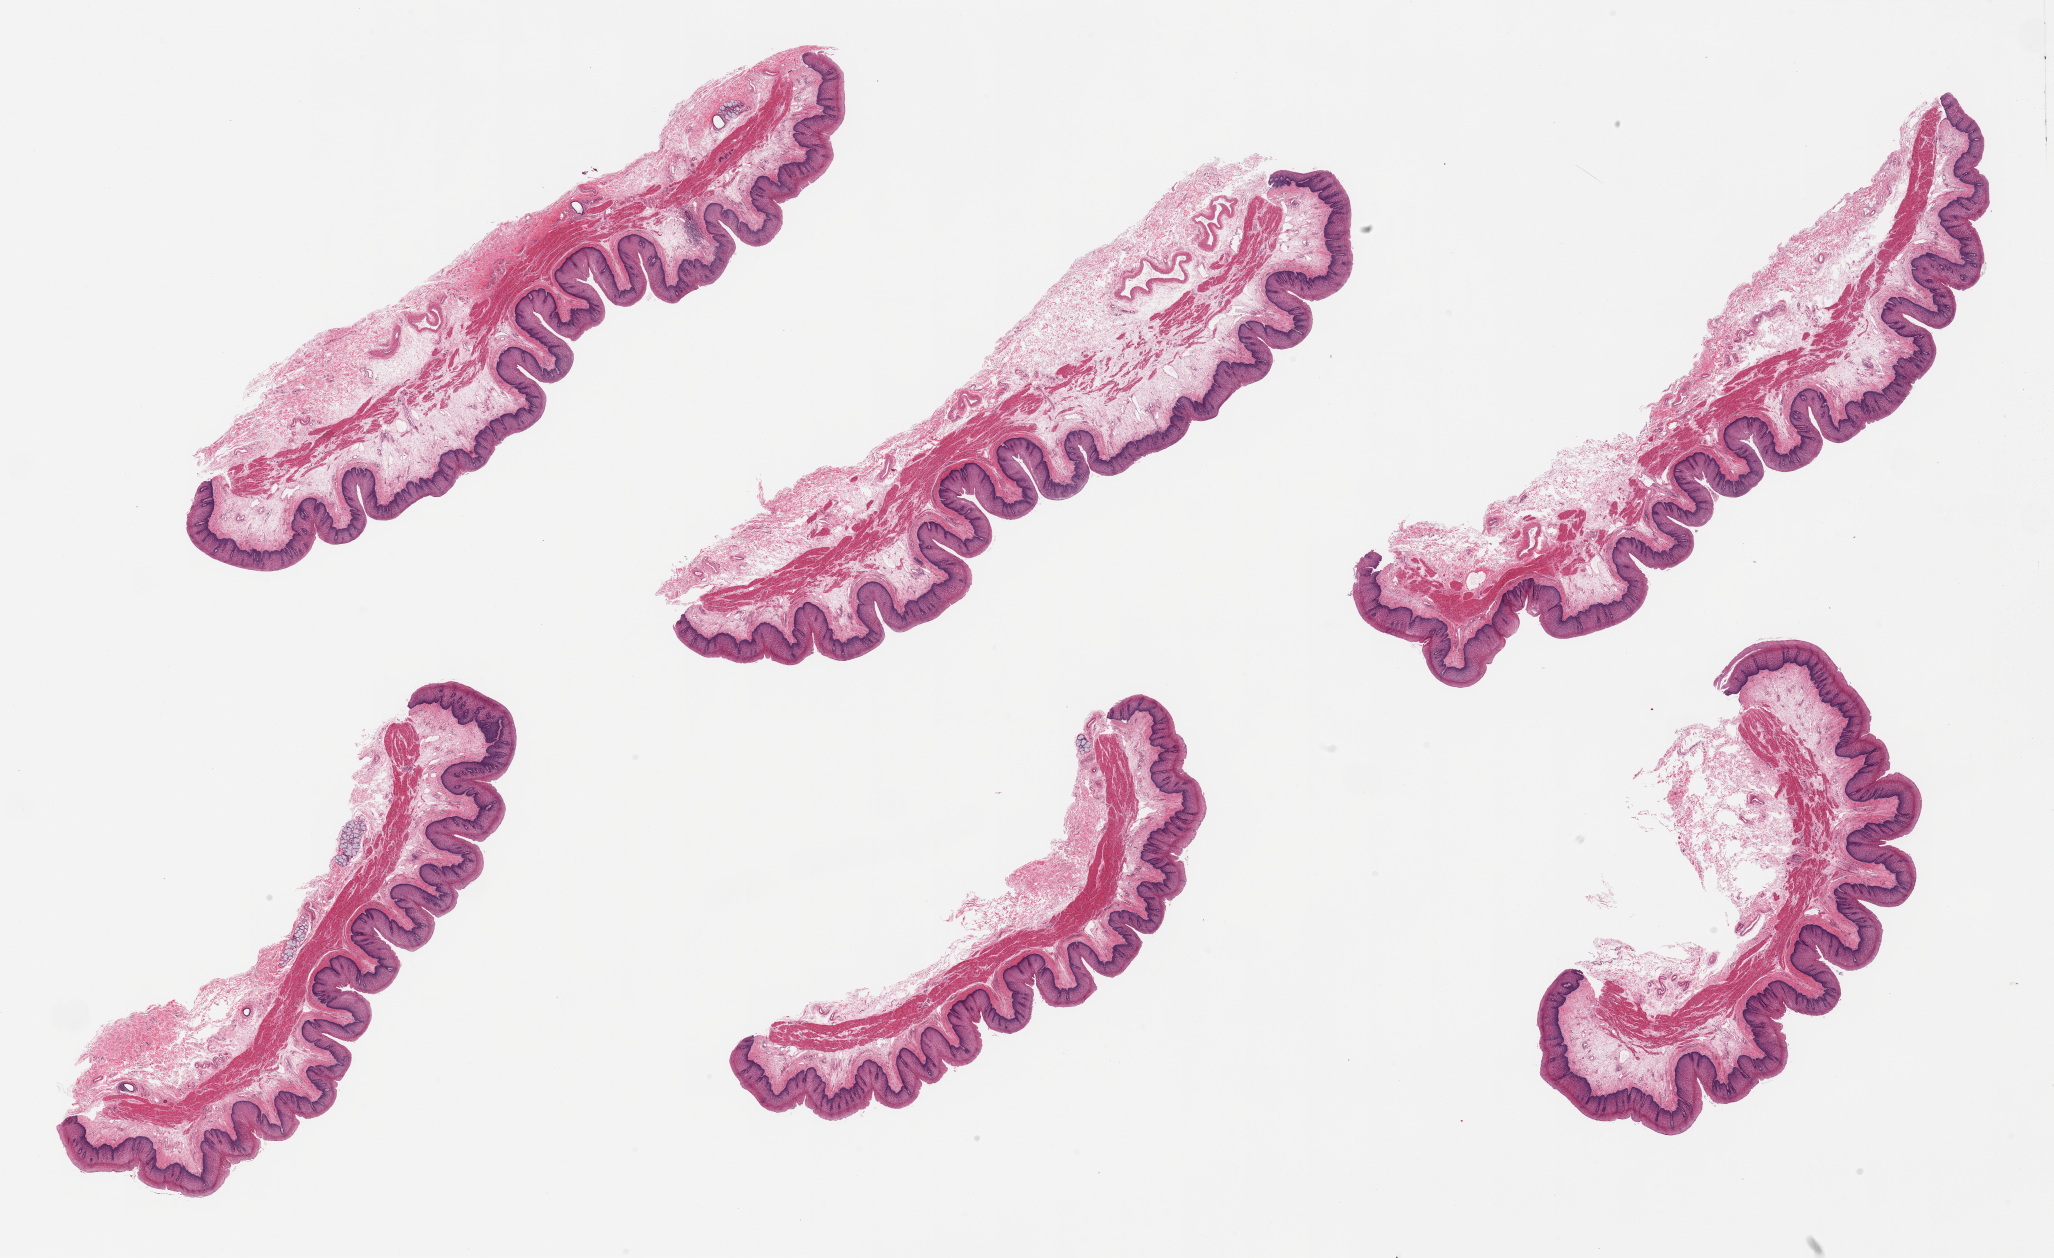
Whole-slide image, hematoxylin and eosin (H&E) stain — low-resolution overview of the scanned area, about 32.5 x 19.9 mm. PAXgene-fixed paraffin-embedded (PFPE) section. Sampled site (target tissue): esophageal mucous membrane. Tissue donor sample. Donor: male.
Pathologist's review note for this sample: 6 pieces; well preserved and well dissected.